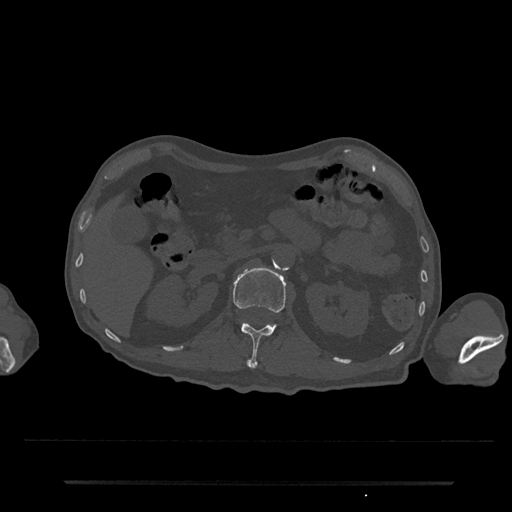
CT including the spine, one axial slice. Position 120 of 797 along the scan axis. Reconstruction kernel Br40s/3. Bone window (W 1800 / L 400 HU). 0.5 mm slice thickness. 512 × 512 image matrix, field of view 427 × 427 mm. Male patient, age 74 years. From the clinical record (not read from this slice): primary cancer: prostate.
Annotated regions visible in this slice (semi-automatically segmented with operator editing):
- L1 vertebra: box from (x=213, y=267) to (x=286, y=369) px